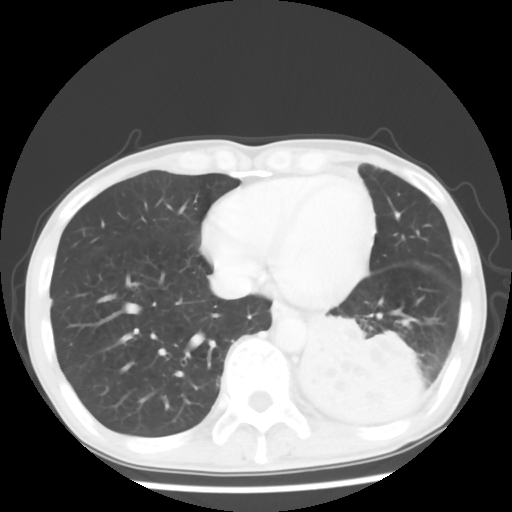
Chest CT, one axial slice. Position 18 of 64 along the scan axis. 120 kVp. Lung window (W 1500 / L -600 HU). 5 mm slice thickness. 512 × 512 image matrix. Patient: male, 68 years. From the clinical record (not read from this slice): clinical TNM (as recorded): T4 N0 M0.
Structures marked on this image (rectangle marked by the reading radiologist):
- lung tumour (recorded histology: squamous cell carcinoma): bounding box <279,307,431,433> (left, top, right, bottom; pixels)